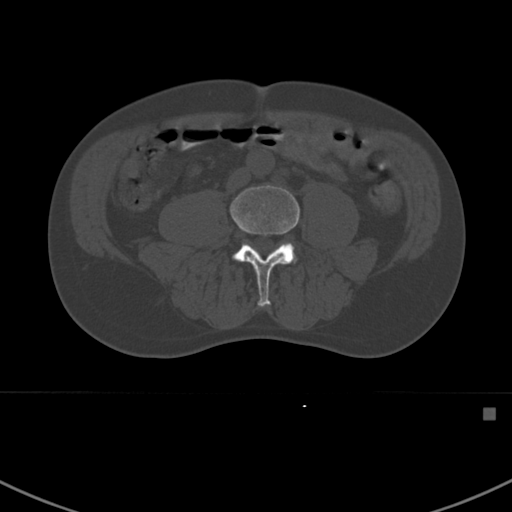
CT including the spine, one axial slice. Position 238 of 412 along the scan axis. Reconstruction kernel Br40s. 120 kVp. Bone window (W 1800 / L 400 HU). 1.5 mm slice thickness. 512 × 512 image matrix, field of view 358 × 358 mm. Patient: male, 59 years. From the clinical record (not read from this slice): primary cancer: prostate.
Structures marked on this image (semi-automatically segmented with operator editing):
- L4 vertebra: bounding box [x1, y1, x2, y2] px = [230, 185, 300, 307]